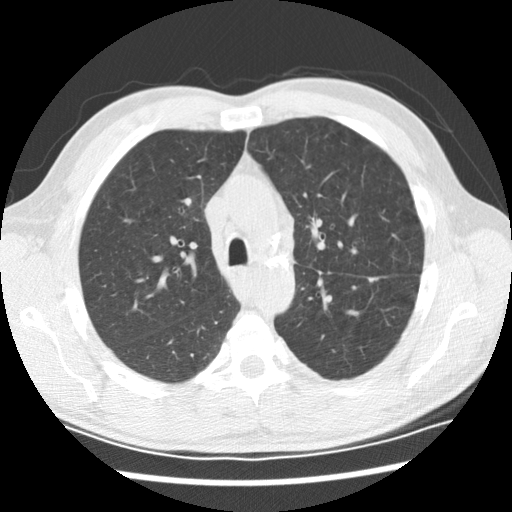
Low-dose screening chest CT, one axial slice. Reconstruction kernel STANDARD. 120 kVp. Lung window (W 1500 / L -600 HU). 2.5 mm slice thickness. 512 × 512 image matrix.
Outlined on this slice (expert manual segmentation):
- lesion 2 (tumor, lower lobe of left lung): bounding box [x1, y1, x2, y2] px = [368, 277, 379, 282]